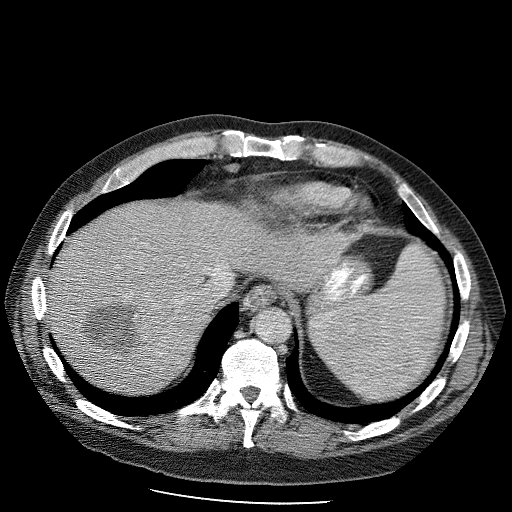
Contrast-enhanced abdominal CT (liver protocol), one axial slice; slice 86 of 98 in the series (ordered by position); reconstruction kernel STANDARD; 120 kVp; soft-tissue window (W 400 / L 40 HU); 512 × 512 image matrix, field of view 400 × 400 mm. Case-level facts recorded for this patient, not image findings: diagnosis: hepatocellular carcinoma (patient treated with transarterial chemoembolisation; whether this scan precedes or follows treatment is not stated here); TNM stage (as recorded): Stage-II; Child-Pugh class: B; tumour nodularity: uninodular.
Outlined on this slice (semi-automatically segmented with operator editing):
- abdominal aorta: bounding box (x1, y1, x2, y2) in pixels: (256, 309, 292, 344)
- liver parenchyma outside the tumour (the mass and vessels are separate outlines, so this box may not span the whole liver): (48, 202, 309, 388)
- mass: (80, 299, 152, 353)